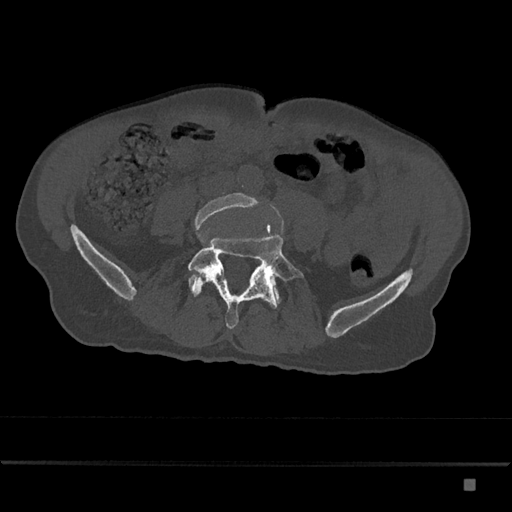
CT including the spine, one axial slice; slice 290 of 797 in the series (ordered by position); reconstruction kernel Br40s/3; 120 kVp; bone window (W 1800 / L 400 HU); 512 × 512 image matrix, field of view 390 × 390 mm. Patient: male, 72 years. From the clinical record (not read from this slice): primary cancer: prostate.
Outlined on this slice (semi-automatic segmentation, software-assisted and operator-edited):
- L4 vertebra: box from (x=194, y=193) to (x=261, y=279) px
- L5 vertebra: (x=188, y=236)–(x=304, y=329)